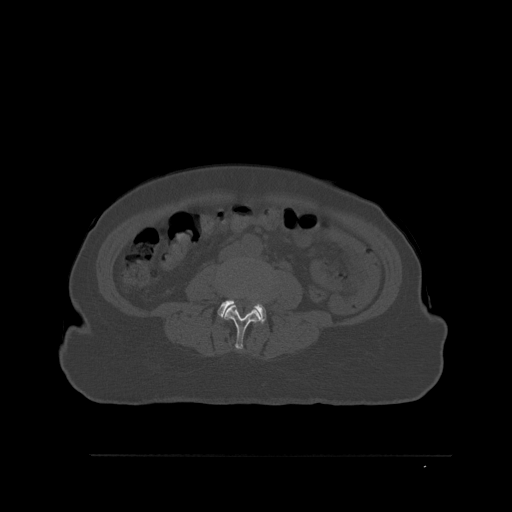
CT including the spine, one axial slice; slice 218 of 527 in the series (ordered by position); bone window (W 1800 / L 400 HU); 512 × 512 image matrix, field of view 470 × 470 mm. Patient: female, 73 years. From the clinical record (not read from this slice): primary cancer: breast; vertebrae with lytic lesions (as recorded): L2.
Structures marked on this image (semi-automatically segmented with operator editing):
- L3 vertebra: box from (x=224, y=297) to (x=268, y=349) px
- L4 vertebra: (x=217, y=294)–(x=266, y=324)